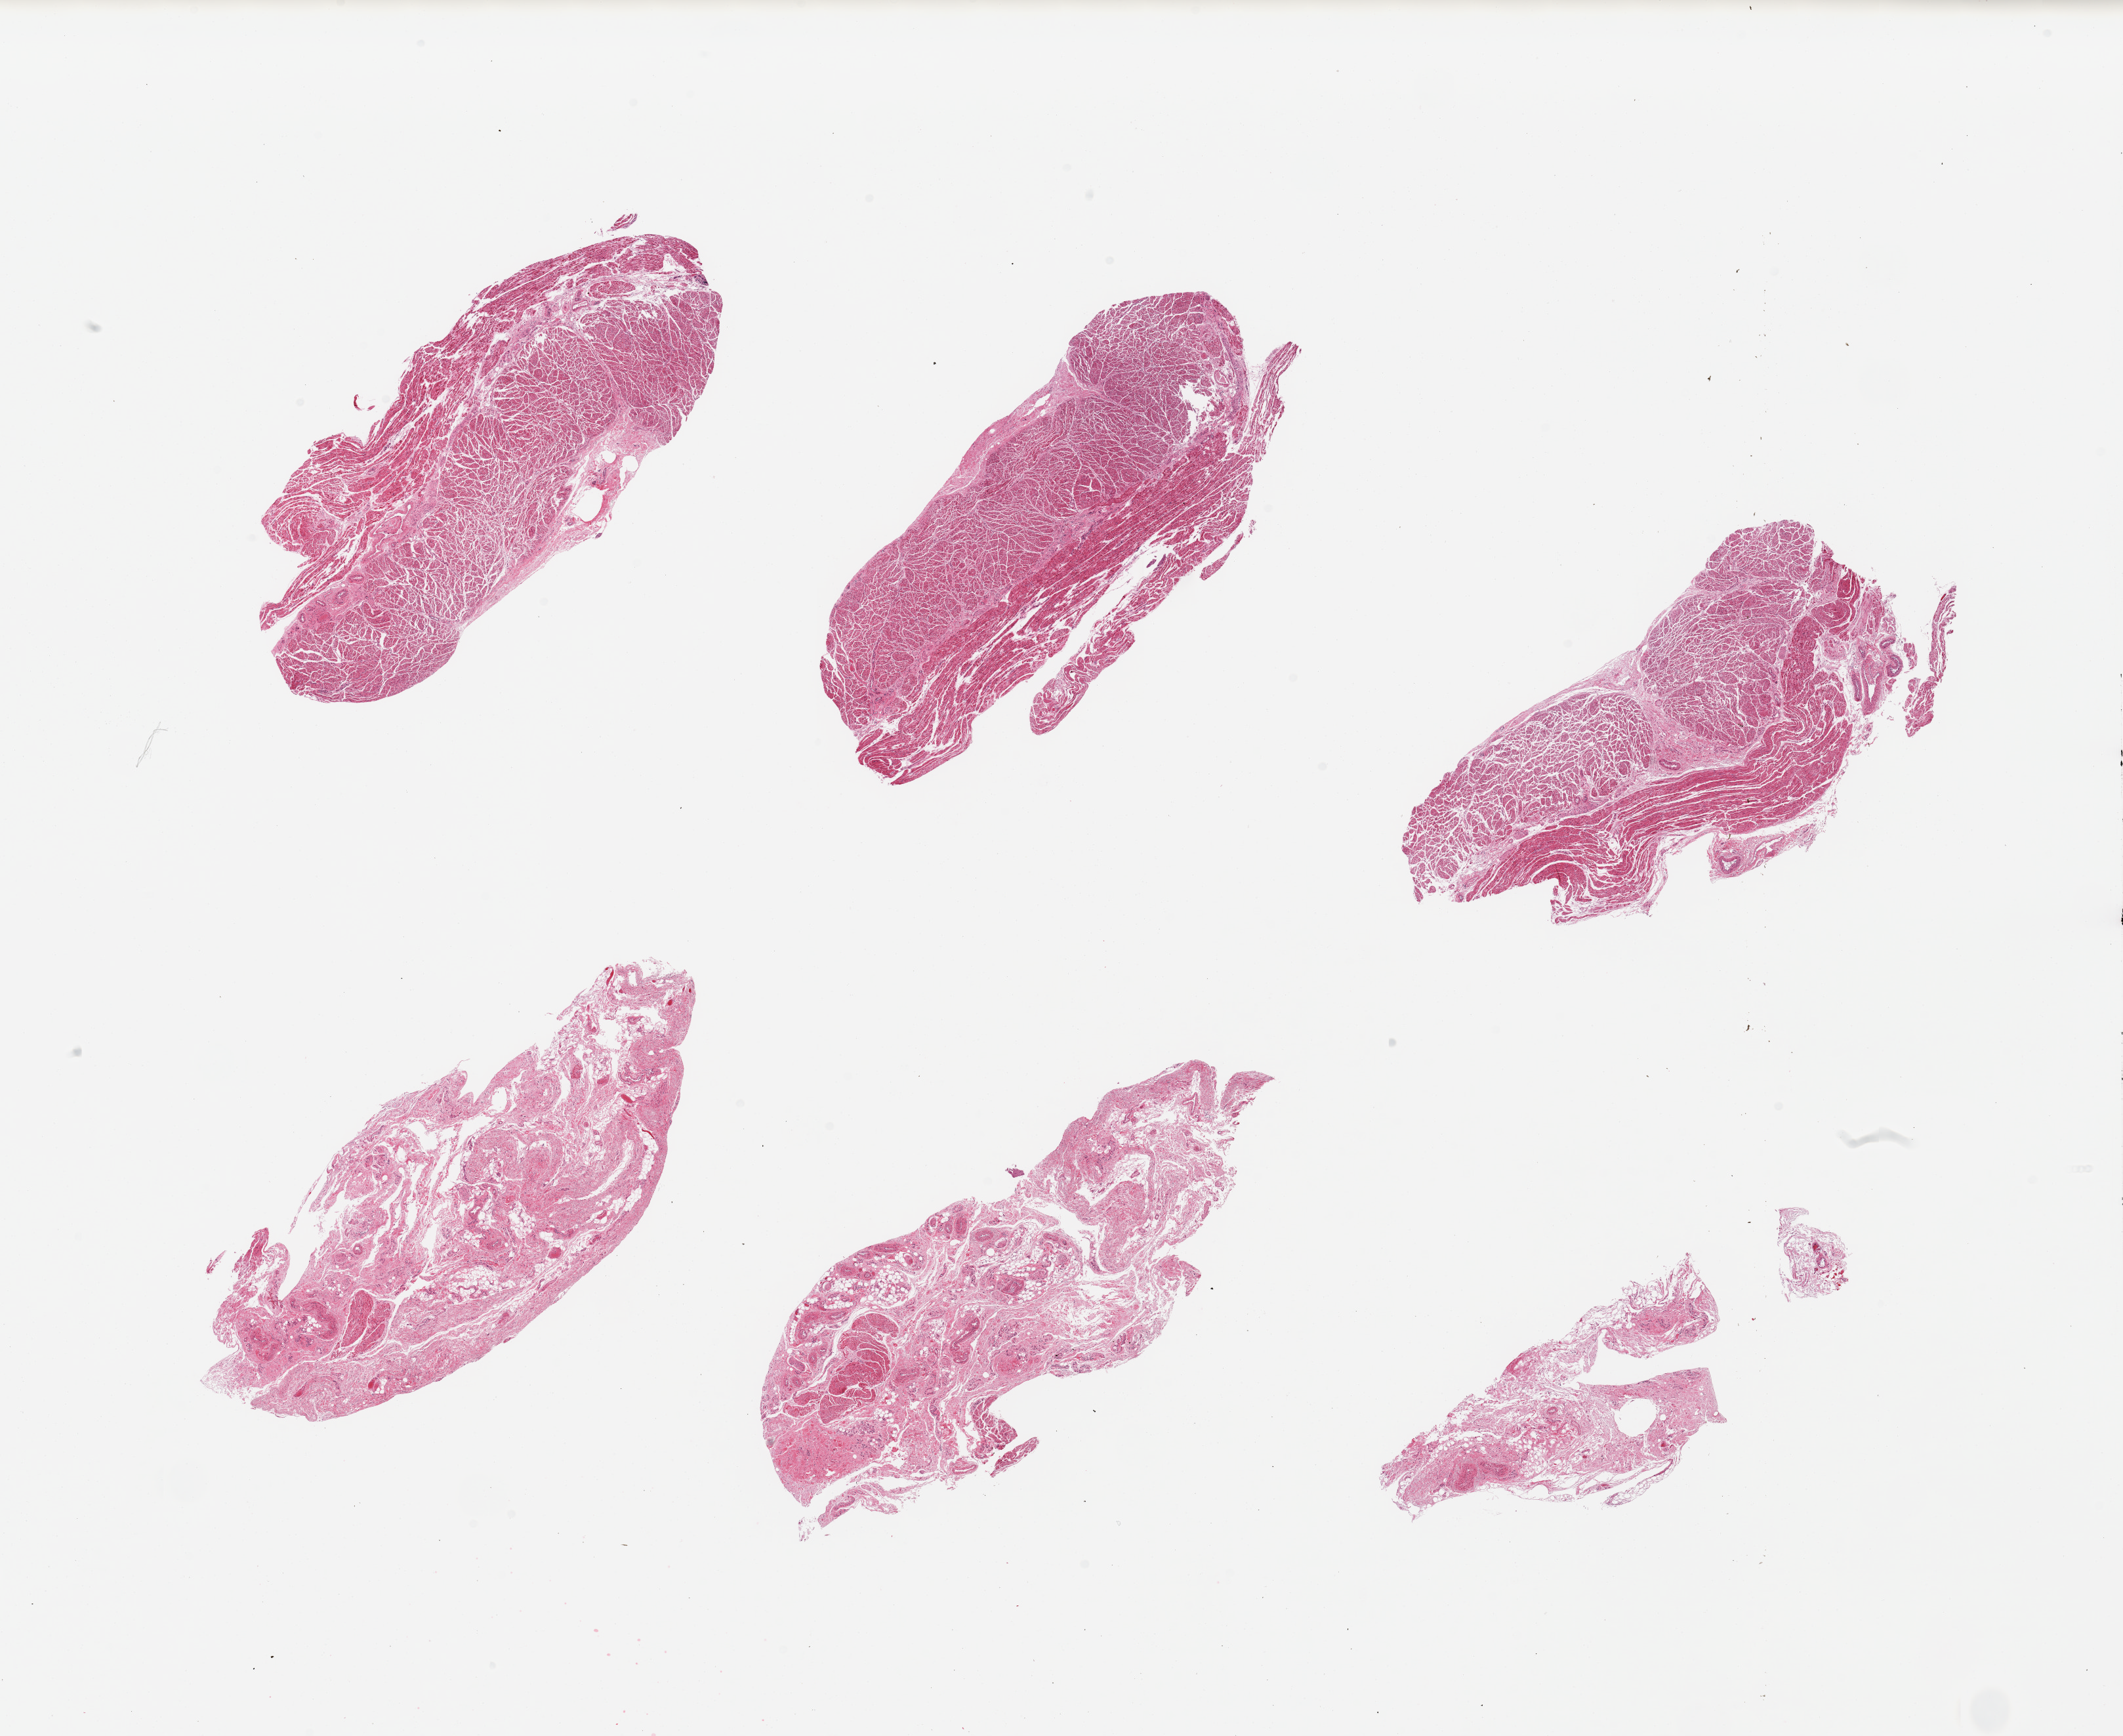
Digitized H&E-stained section — low-resolution overview of the scanned area, about 25.6 x 20.9 mm; PAXgene-fixed paraffin-embedded (PFPE) section; sampled site (target tissue): gastroesophageal junction; donor tissue sample. Donor: female.
- reviewer comment on this tissue sample: 6 pieces; 3 have muscle, 3 have >90% fibrovascular fatty stroma